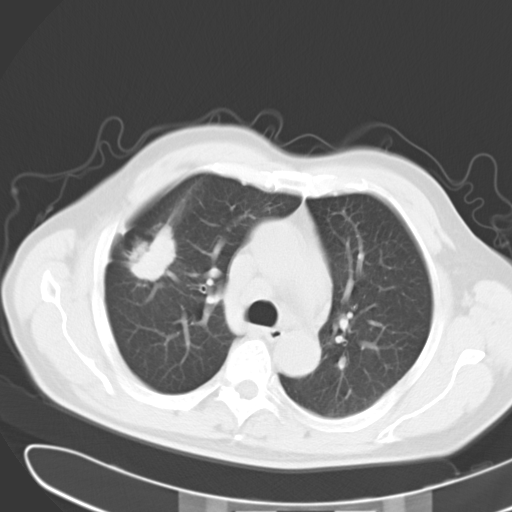
Chest CT, one axial slice; slice 21 of 31 in the series (ordered by position); reconstruction kernel B40f; lung window (W 1500 / L -600 HU); 10 mm slice thickness; 512 × 512 image matrix, field of view 364 × 364 mm. Patient: male, 59 years. Case-level facts recorded for this patient, not image findings: clinical TNM (as recorded): T2 N3 M0.
Outlined on this slice (bounding box drawn by a radiologist):
- lung tumour (recorded histology: adenocarcinoma): bounding box <125,221,178,283> (left, top, right, bottom; pixels)